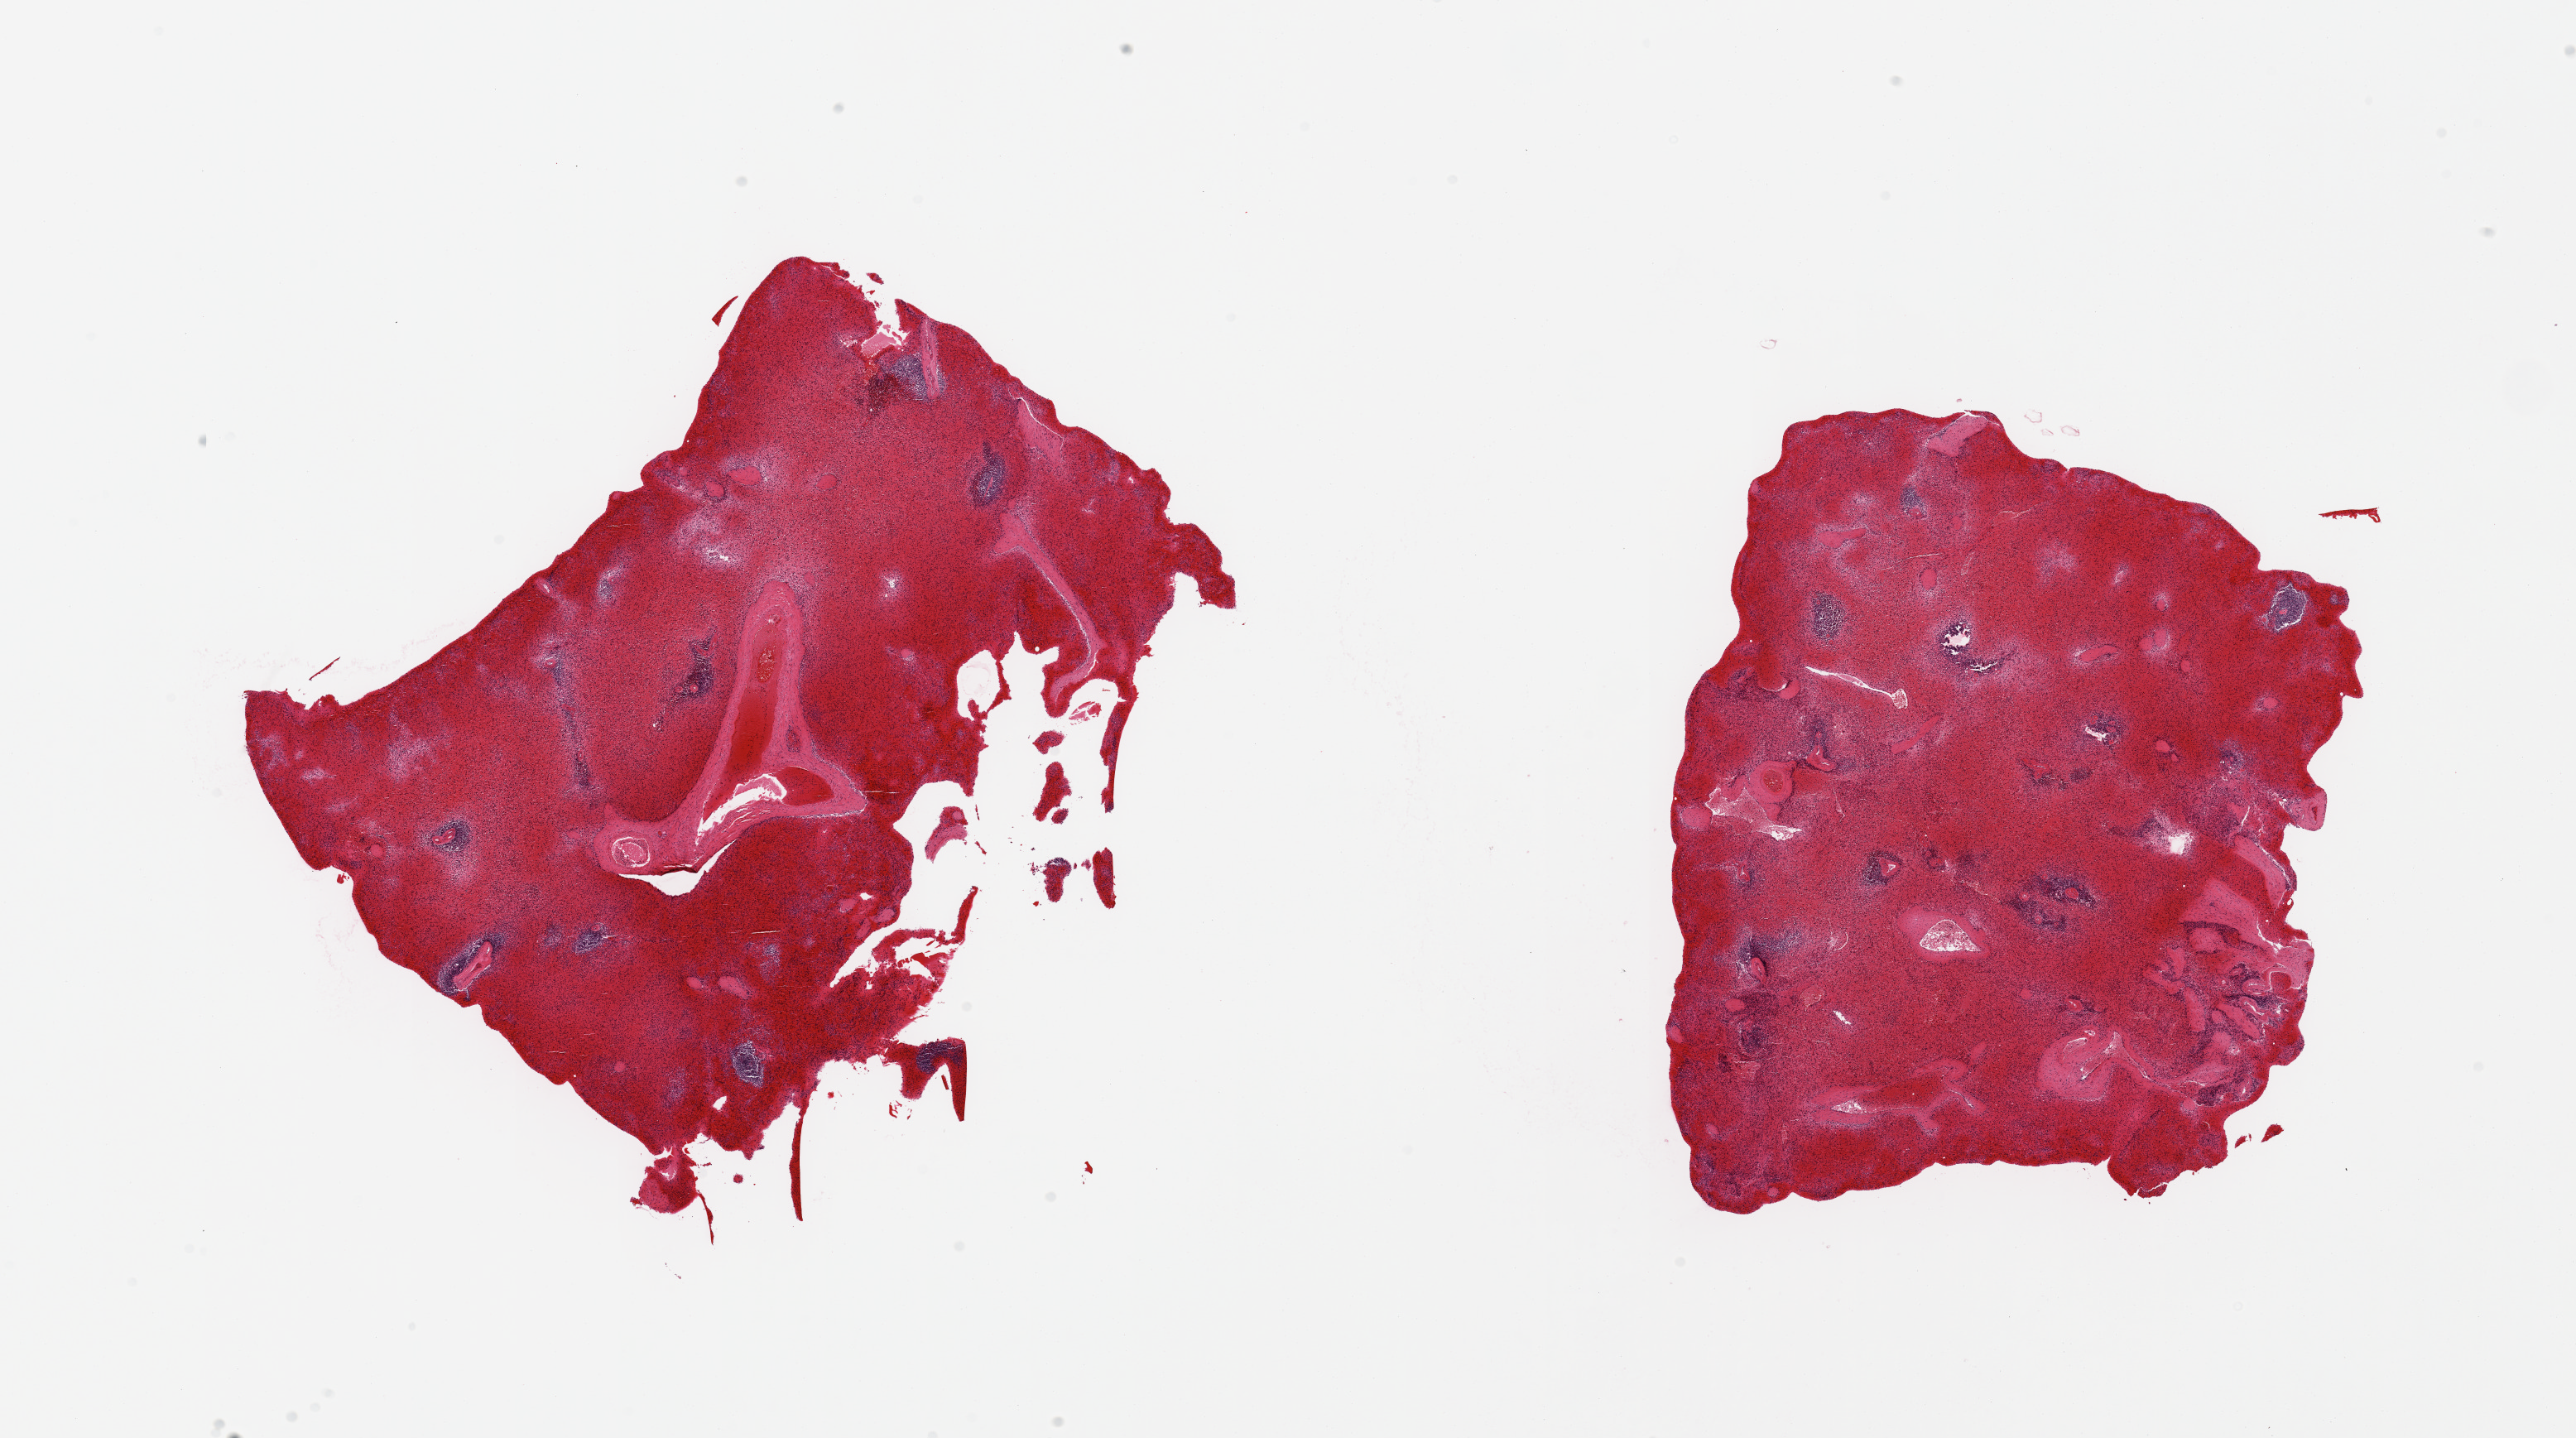
Haematoxylin and eosin whole-slide image — low-resolution overview of the scanned area, about 24.6 x 13.7 mm. PAXgene-fixed, paraffin-embedded tissue. Section of spleen (target tissue). Tissue donor sample. Donor: female.
- review note (as recorded): 2 pieces; severe congestion